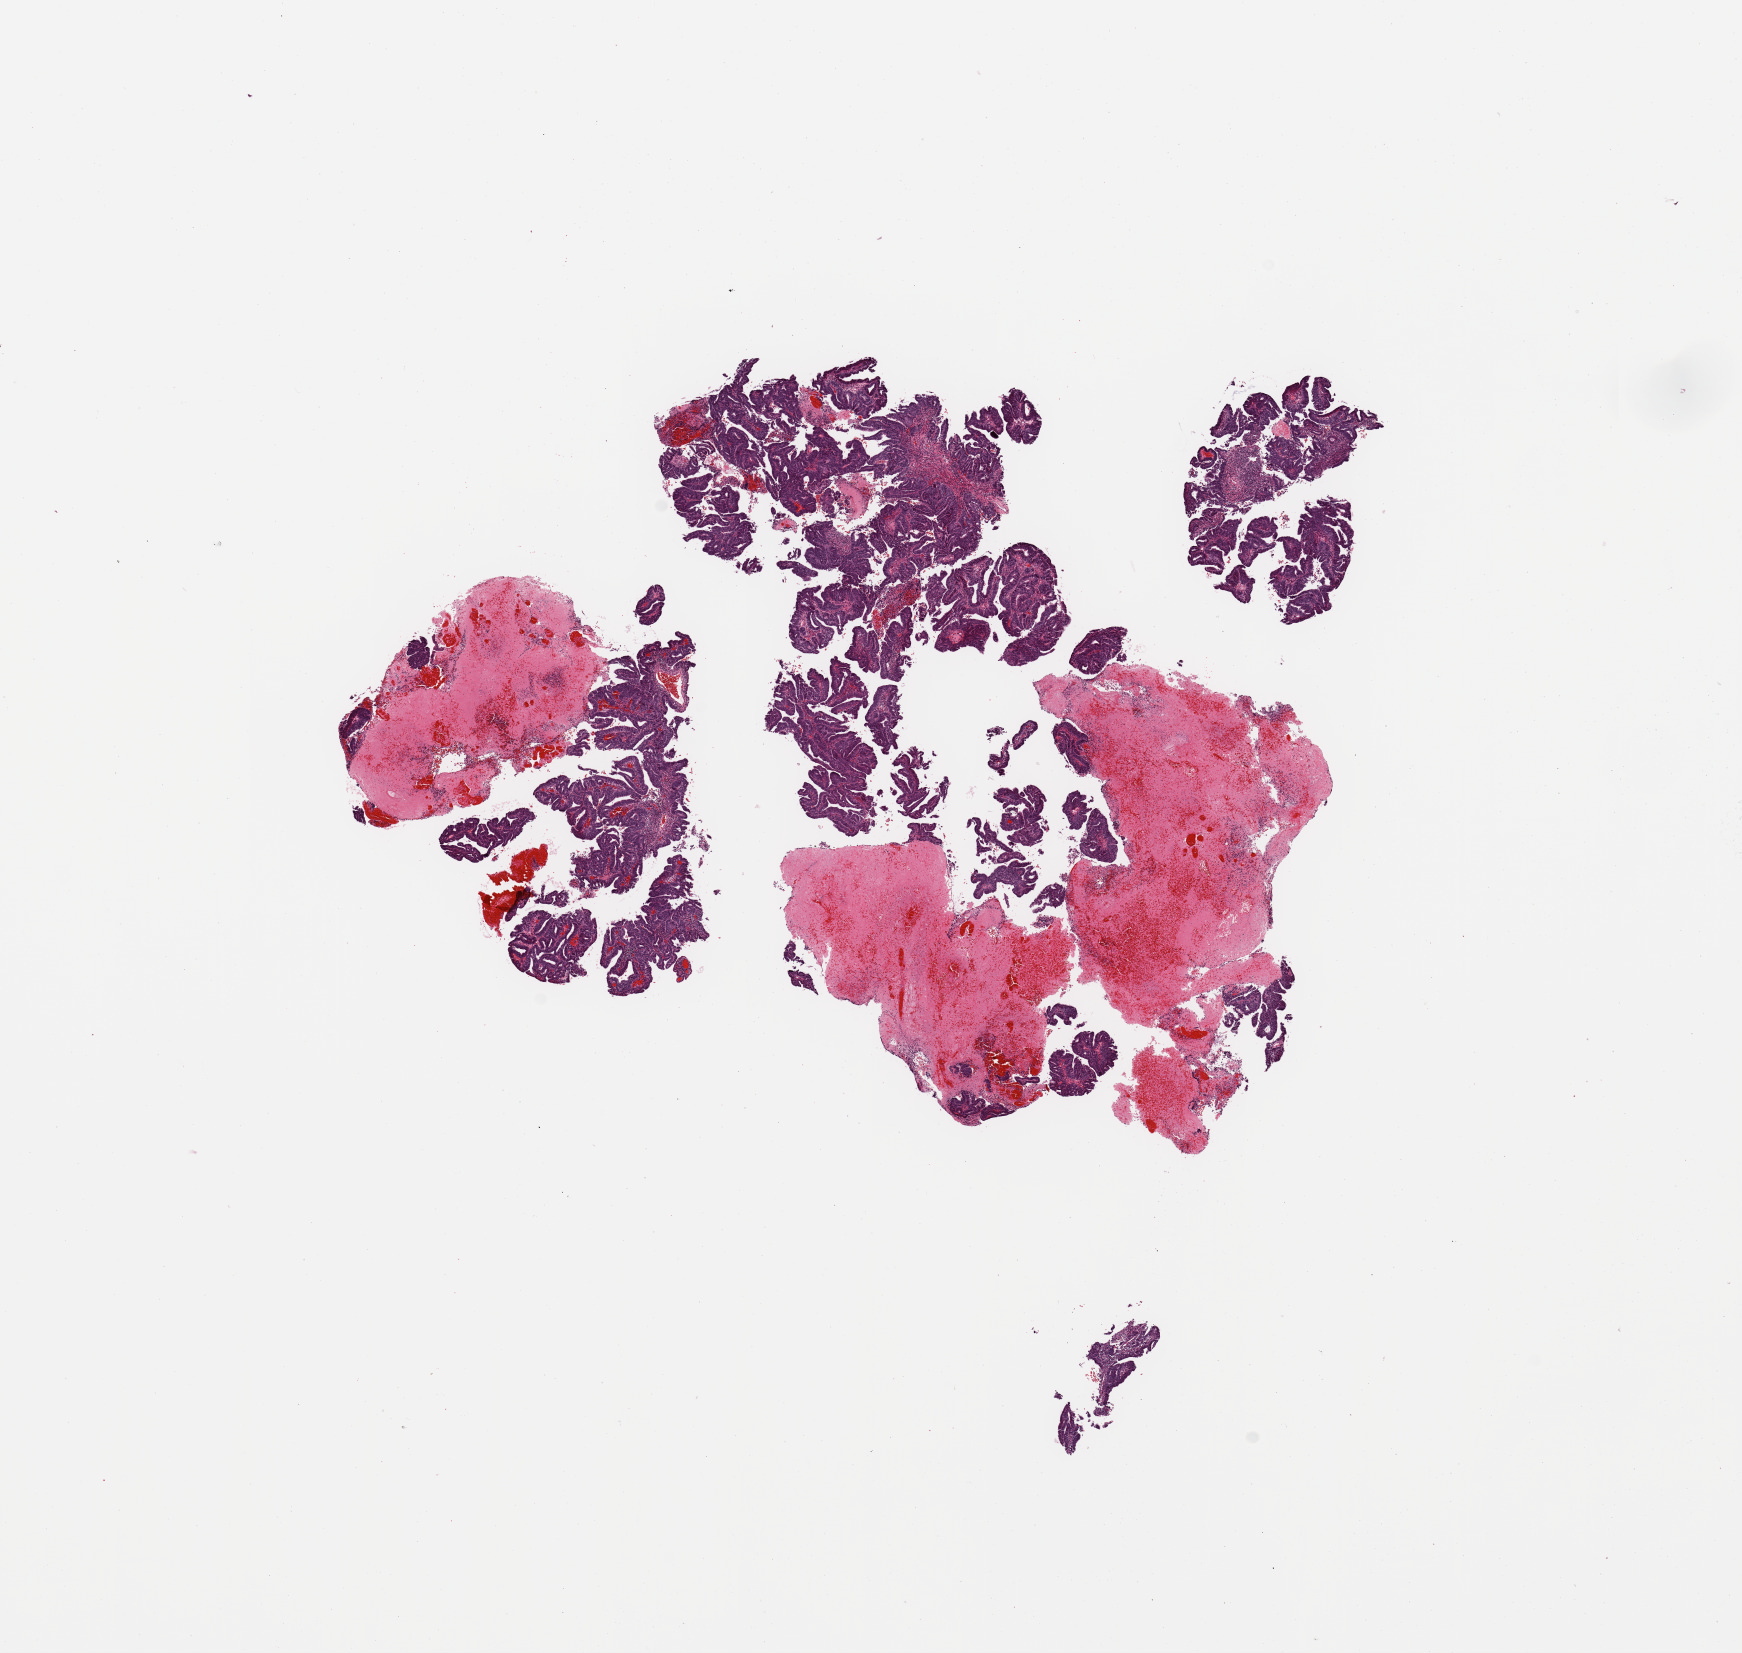
H&E whole-slide image — a low-resolution overview of the entire scanned area, about 13.8 x 13.1 mm, tumour tissue sample, uterus. 57-year-old female patient. Histologic grade: G1 (well differentiated).
AJCC pathologic stage: I. Histologic diagnosis: Endometrioid adenocarcinoma, NOS.